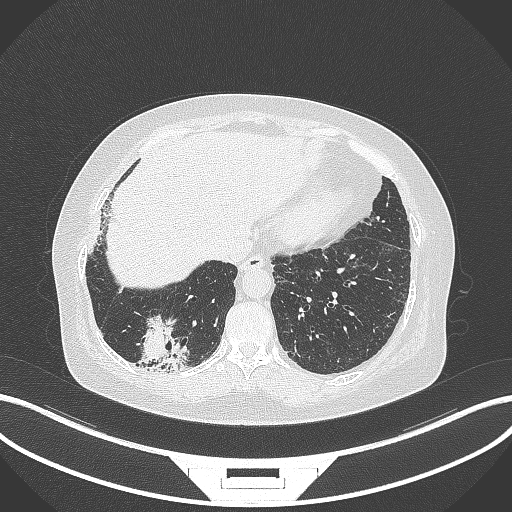
Chest CT, one axial slice; slice 40 of 296 in the series (ordered by position); 120 kVp; lung window (W 1500 / L -600 HU); 512 × 512 image matrix. Female patient, age 65 years. From the clinical record (not read from this slice): clinical TNM (as recorded): T2b N1 M0.
Annotated regions visible in this slice (bounding box drawn by a radiologist):
- lung tumour (recorded histology: adenocarcinoma): bounding box [x1, y1, x2, y2] px = [135, 313, 192, 374]